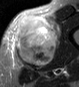
MRI of an extremity soft-tissue mass, one axial slice; slice 22 of 45 in the series (ordered by position); STIR; MR volume resampled by the dataset authors to the PET/CT grid (not the native acquisition matrix); 79 × 87 image matrix. Male patient. Case-level facts recorded for this patient, not image findings: histological type: pleiomorphic leiomyosarcoma; grade: high; site of the primary tumour: left thigh.
Annotated regions visible in this slice (expert contour drawn on MRI and transferred to this co-registered scan by the dataset authors):
- gross tumour volume including surrounding oedema: box from (x=13, y=16) to (x=60, y=67) px
- gross tumour volume (mass): (x=13, y=16)–(x=55, y=67)